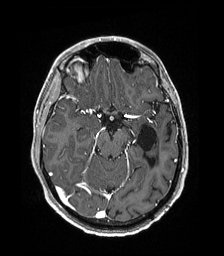
Brain MRI from a brain-tumour surgery series, one axial slice; position 113 of 192 along the scan axis; T1-weighted post-contrast; 224 × 256 image matrix, field of view 224 × 256 mm. Case-level facts recorded for this patient, not image findings: histopathology: Low grade glioma; IDH mutation: no; tumour location: Left Parieto-Occipital Intraventricular.
Structures marked on this image (expert manual segmentation):
- previous resection cavity: bounding box [x1, y1, x2, y2] px = [137, 125, 157, 167]